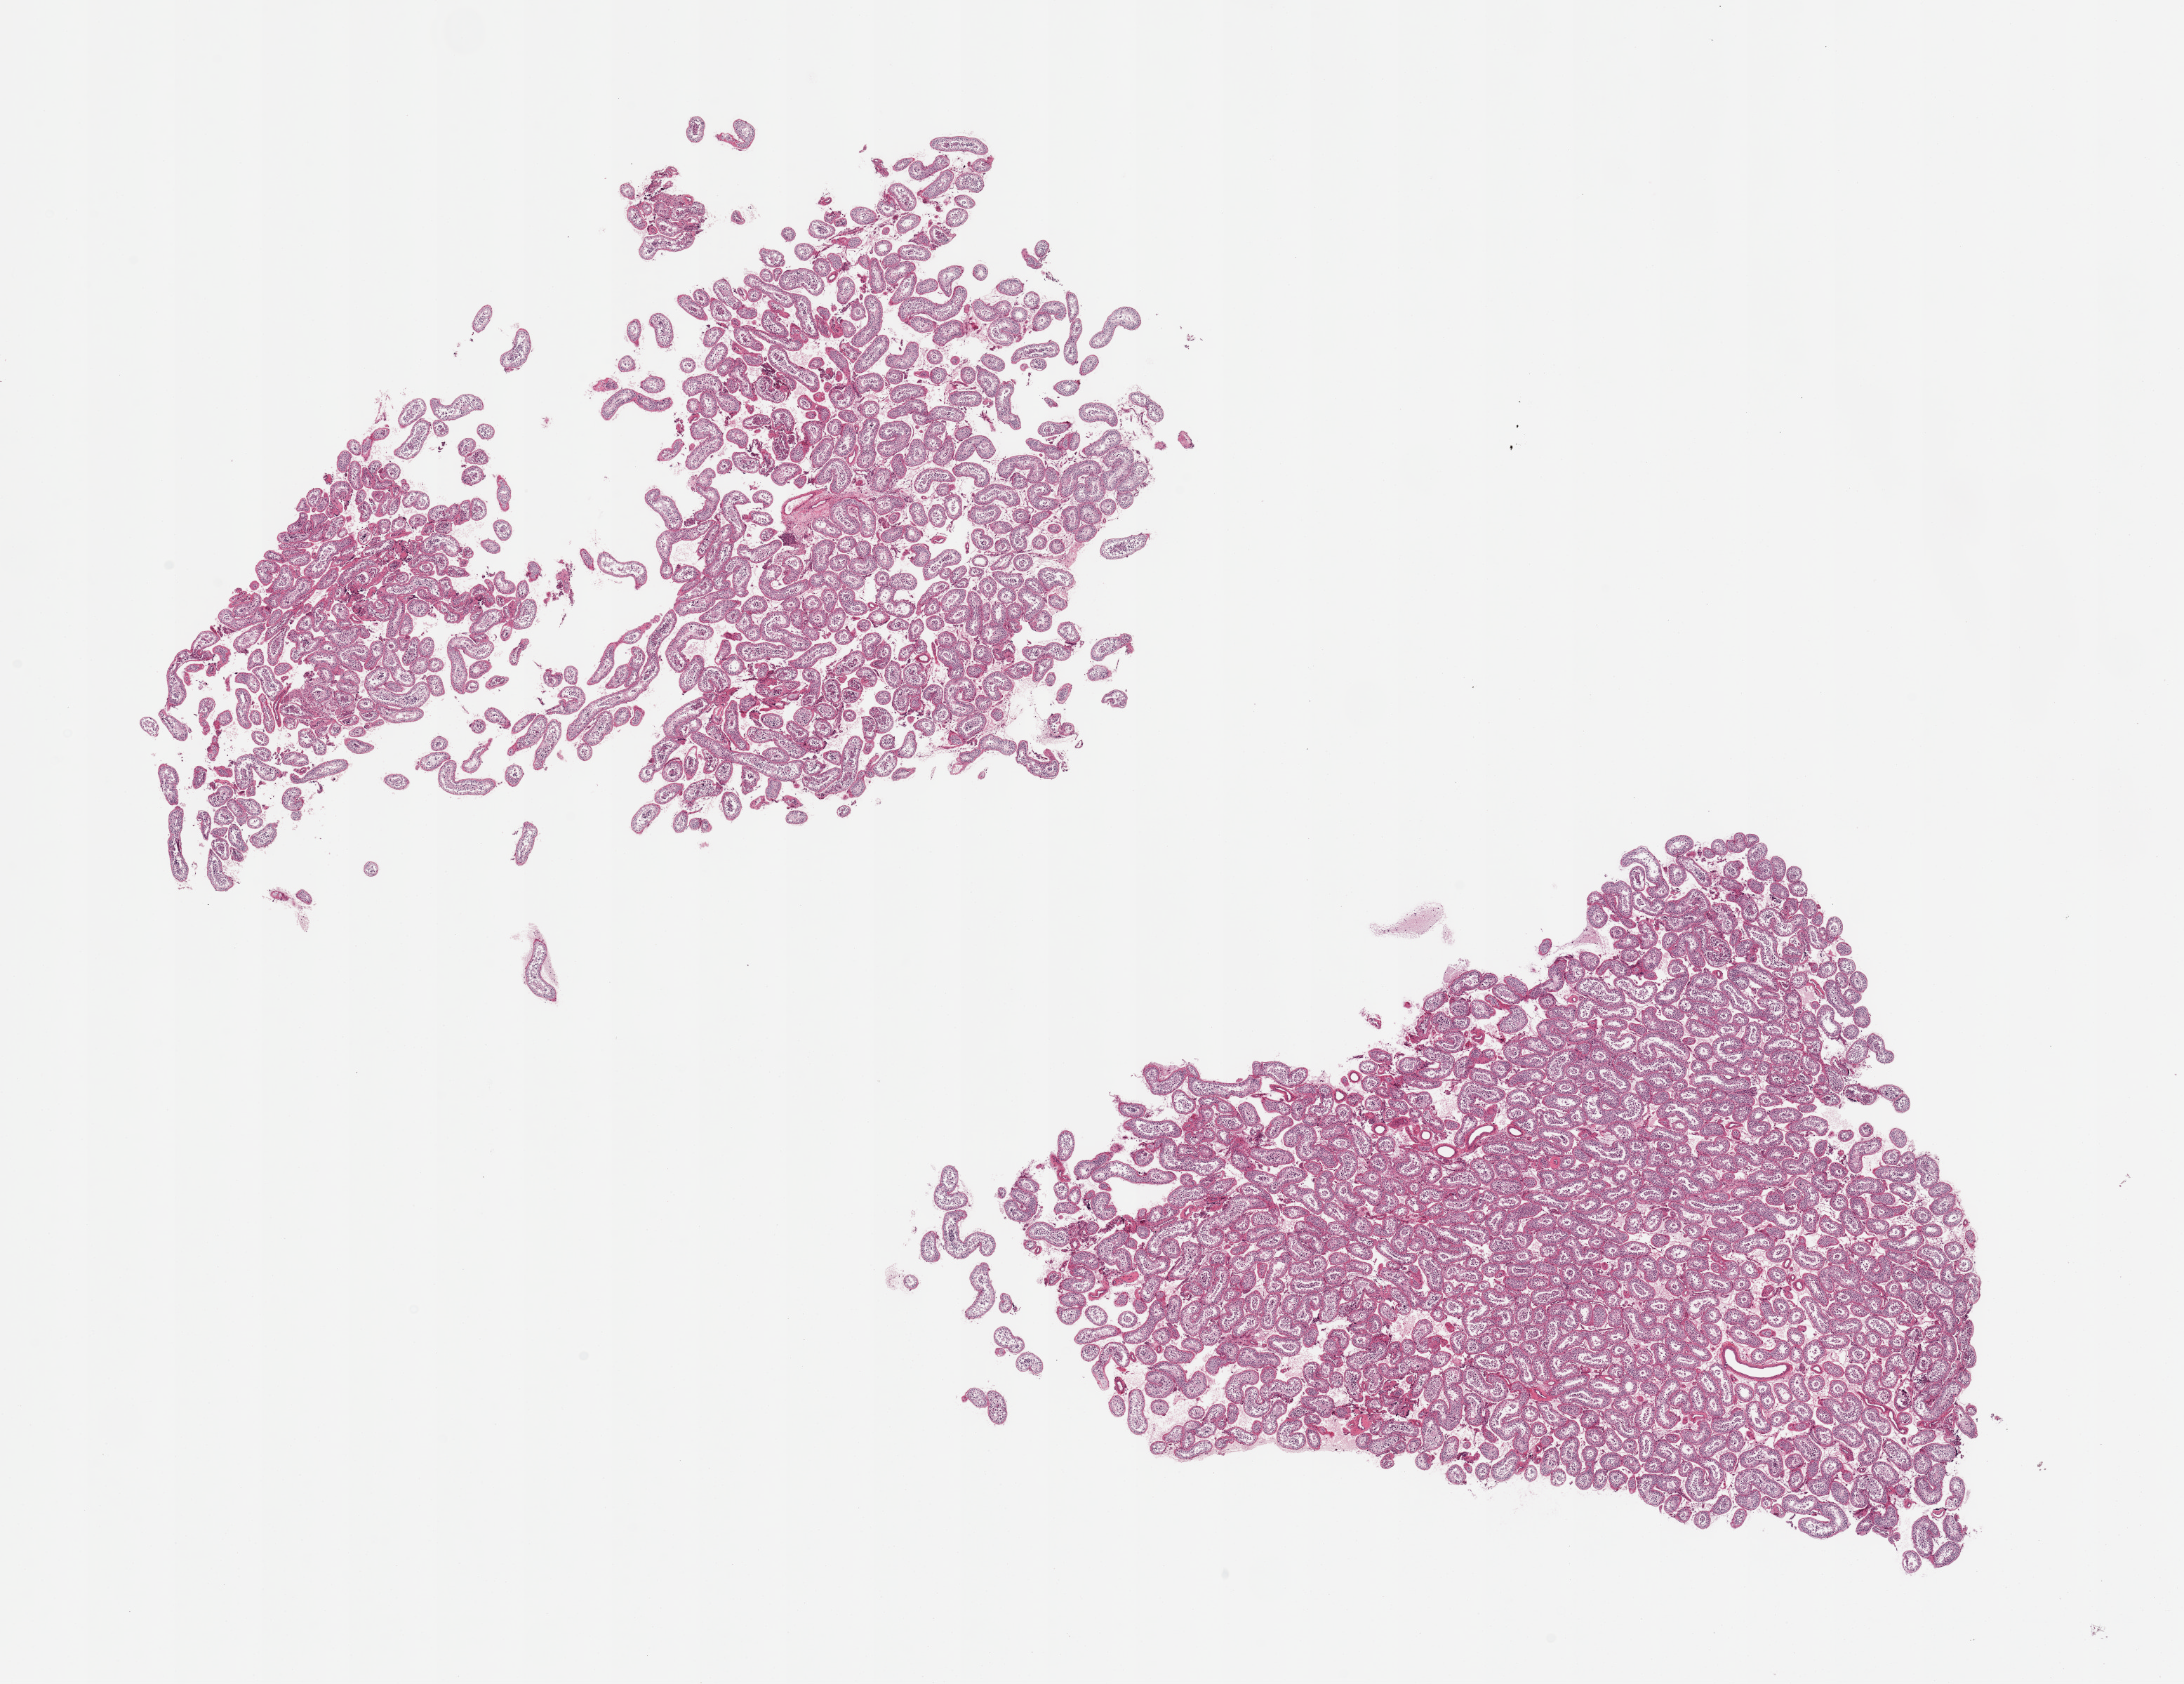
Haematoxylin and eosin whole-slide image, low-resolution overview of the scanned area, about 24.6 x 19.0 mm (from a 20x scan). PAXgene-fixed, paraffin-embedded tissue. Target tissue: testis. Tissue donor sample. Male donor.
- reviewer comment on this tissue sample: 2 pieces. spermatogenesis